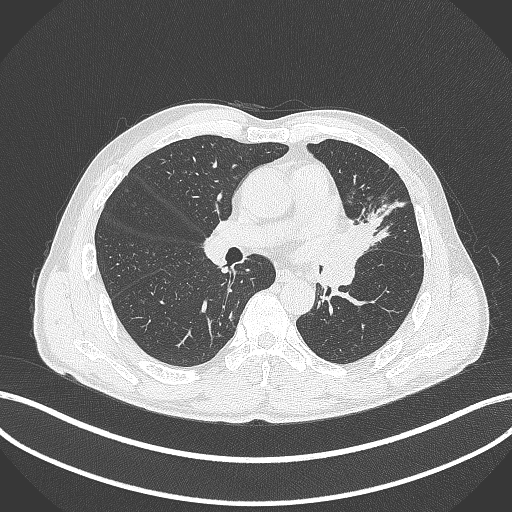
Chest CT, one axial slice. Position 230 of 429 along the scan axis. Reconstruction kernel B70f. Lung window (W 1500 / L -600 HU). 512 × 512 image matrix, field of view 400 × 400 mm. Male patient, age 57 years. From the clinical record (not read from this slice): clinical TNM (as recorded): T2b N0 M0.
Structures marked on this image (bounding box drawn by a radiologist):
- lung tumour (recorded histology: squamous cell carcinoma): bounding box <339,208,383,275> (left, top, right, bottom; pixels)